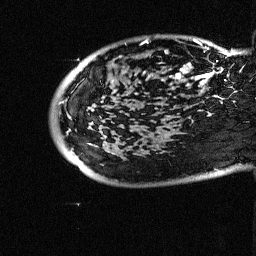
Breast MRI (dynamic contrast-enhanced), one sagittal slice; slice 11 of 64 in the series (ordered by position); dynamic contrast-enhanced study with each time point stored as its own series, time point 2 of 3 at this slice position (early post-contrast, ordered by acquisition time); 1.5 T; TE 4.5 ms, TR 11 ms; 256 × 256 image matrix, field of view 200 × 200 mm. Patient: female, 38 years. Case-level facts recorded for this patient, not image findings: setting: breast cancer imaged before/during neoadjuvant chemotherapy; receptor status: HR-positive, HER2-negative.
Annotated regions visible in this slice (semi-automatic segmentation, software-assisted and operator-edited):
- analysis volume of interest (the breast-tissue region the enhancement analysis was run in; not a lesion): bounding box (x1, y1, x2, y2) in pixels: (88, 19, 252, 126)
- tumour enhancement mask (voxels above the 90 % enhancement threshold inside the analysis volume of interest): (146, 40, 210, 83)